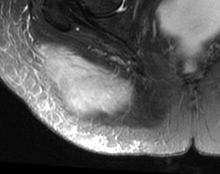
MRI of an extremity soft-tissue mass, one axial slice; position 17 of 63 along the scan axis; T2-weighted fat-saturated; MR volume resampled by the dataset authors to the PET/CT grid (not the native acquisition matrix); 3.27 mm slice thickness; 220 × 174 image matrix, field of view 215 × 170 mm. Female patient. From the clinical record (not read from this slice): histological type: spindle cell suggestive of myxofibrosarcoma; grade: intermediate; site of the primary tumour: right buttock.
Annotated regions visible in this slice (expert contour drawn on MRI and transferred to this co-registered scan by the dataset authors):
- gross tumour volume (mass): bounding box [x1, y1, x2, y2] px = [38, 43, 135, 117]